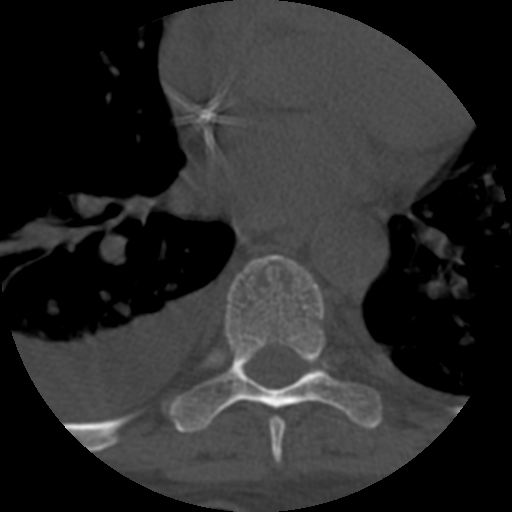
CT including the spine, one axial slice. Position 399 of 708 along the scan axis. 120 kVp. One of 3 acquisitions stored at this slice position. Bone window (W 1800 / L 400 HU). 1.25 mm slice thickness. 512 × 512 image matrix, field of view 160 × 160 mm. Patient age 55 years. From the clinical record (not read from this slice): primary cancer: colon; vertebrae with lytic lesions (as recorded): T12, L1, L5.
Structures marked on this image (semi-automatic segmentation, software-assisted and operator-edited):
- T7 vertebra: bounding box (x1, y1, x2, y2) in pixels: (269, 417, 286, 464)
- T8 vertebra: (173, 254, 382, 434)